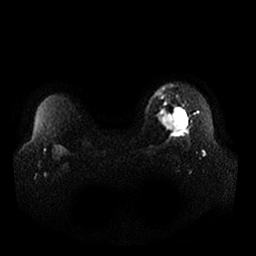
Breast MRI, one axial slice; position 26 of 32 along the scan axis; diffusion-weighted series; image 2 of 4 stored at this slice position (different b-values; order by instance number); 1.5 T; 4 mm slice thickness; 256 × 256 image matrix. Female patient.
Outlined on this slice (outlined manually by an expert reader):
- tumour on diffusion-weighted imaging: bounding box [x1, y1, x2, y2] px = [173, 108, 187, 133]